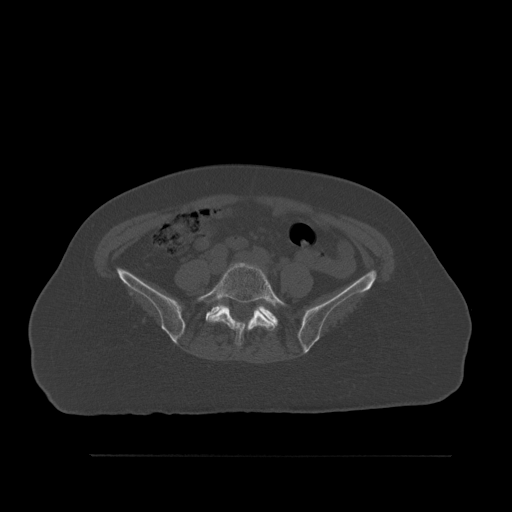
CT including the spine, one axial slice; slice 187 of 527 in the series (ordered by position); bone window (W 1800 / L 400 HU); 1.5 mm slice thickness; 512 × 512 image matrix, field of view 470 × 470 mm. Female patient, age 73 years. Case-level facts recorded for this patient, not image findings: primary cancer: breast.
Structures marked on this image (semi-automatic segmentation, software-assisted and operator-edited):
- L5 vertebra: box from (x=197, y=262) to (x=287, y=346) px